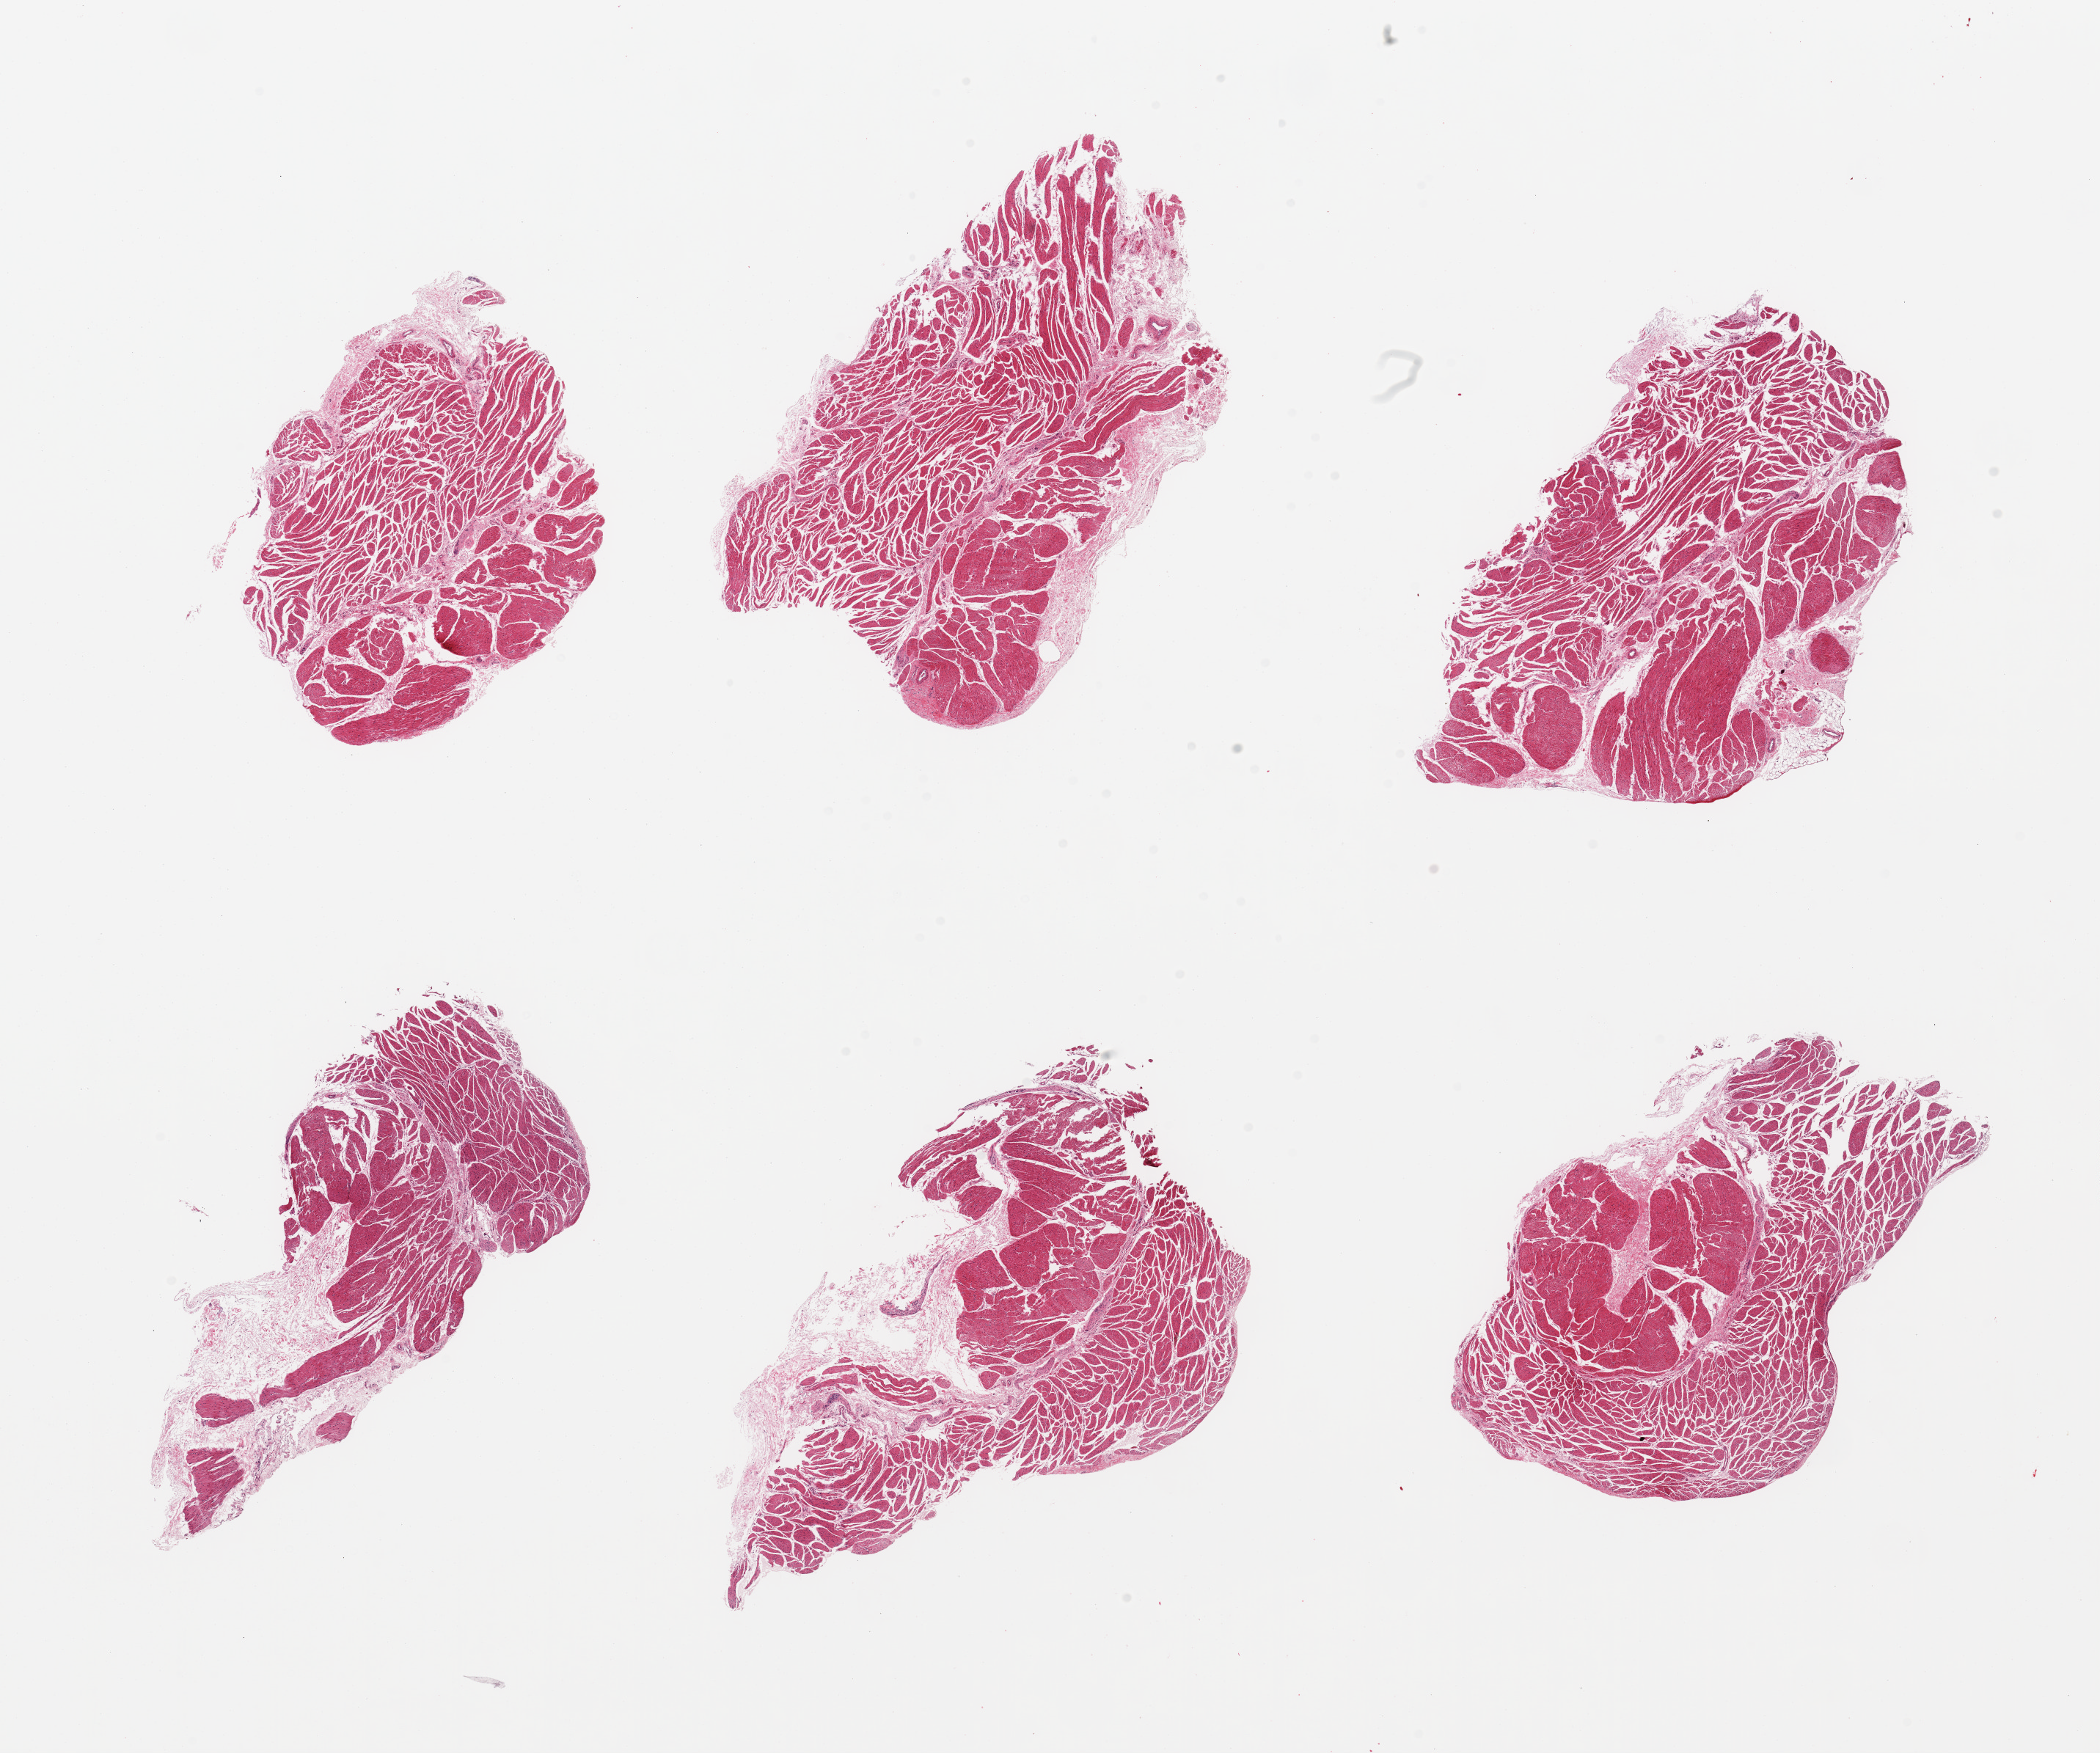
Hematoxylin and eosin (H&E) whole-slide image — low-resolution overview of the scanned area, about 22.6 x 18.9 mm (from a 20x scan). PAXgene-fixed paraffin-embedded (PFPE) section. Target tissue: esophageal muscle. Tissue donor sample. Male donor.
- reviewer comment on this tissue sample: 6 pieces